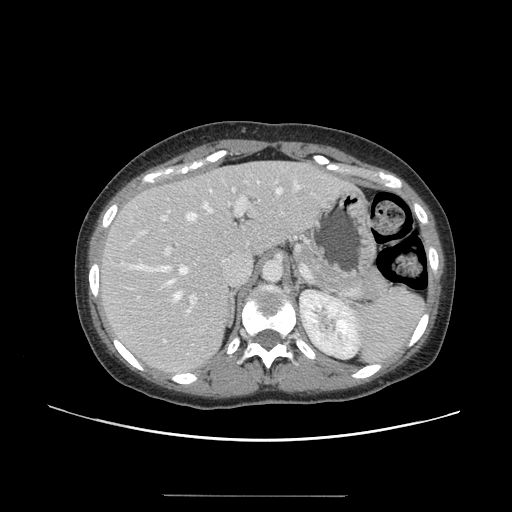
Contrast-enhanced abdominal CT, one axial slice. Slice 97 of 144 in the series (ordered by position). 120 kVp. Soft-tissue window (W 400 / L 40 HU). 2.5 mm slice thickness. 512 × 512 image matrix, field of view 380 × 380 mm. Female patient, age 53 years. Case-level facts recorded for this patient, not image findings: diagnosis: colorectal cancer liver metastases, imaged before liver resection; multiple liver metastases: yes; largest metastasis: 1.1 cm.
Annotated regions visible in this slice (manually delineated by an expert):
- hepatic veins: bounding box <132,186,300,300> (left, top, right, bottom; pixels)
- liver: <98,162,344,375>
- planned liver remnant (the part of the liver to remain after resection): <99,162,307,300>
- portal vein (with intrahepatic branches): <138,180,278,317>